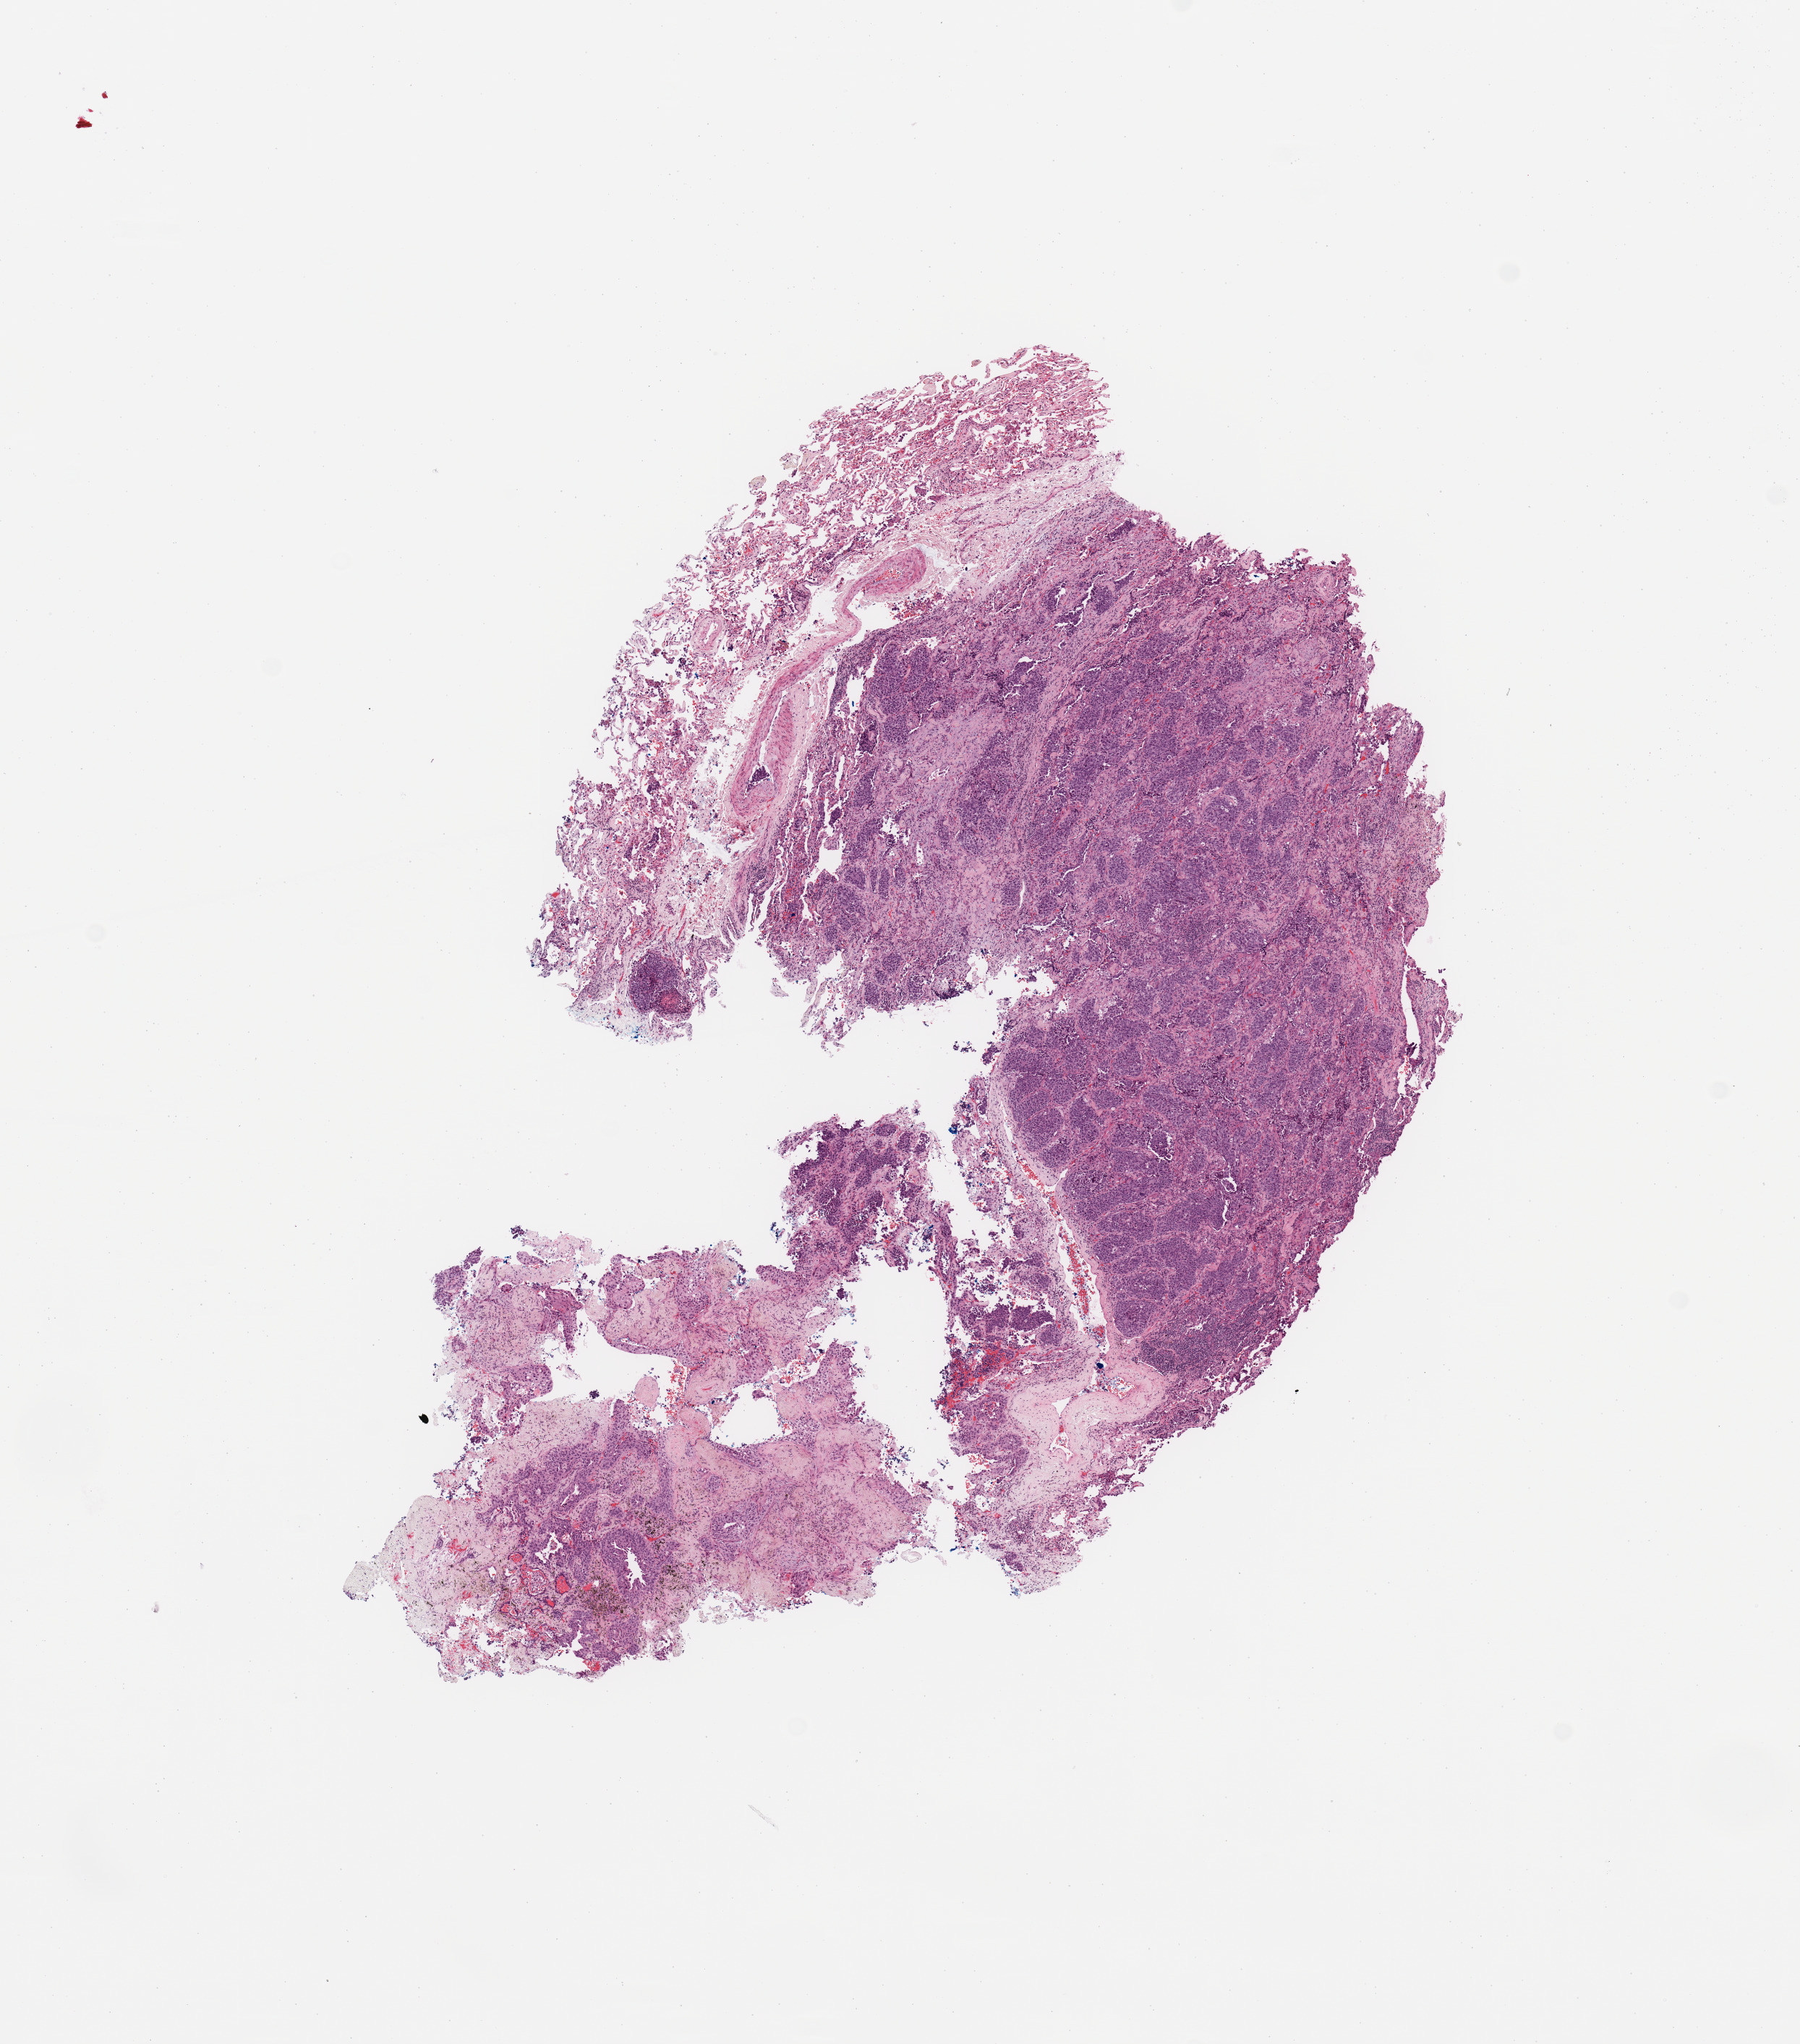
Digitized H&E-stained tissue section (whole slide), shown as a low-resolution overview of the whole scanned area (about 9.8 x 11.2 mm), tumour tissue sample, sampled site: lung. Patient: female, age 73 years. Histologic grade: G3 (poorly differentiated). Slide review estimates, as recorded: tumour nuclei 70%, necrosis 10%.
- primary tumour site (as recorded): right upper lobe
- histologic diagnosis: Squamous cell carcinoma, NOS
- AJCC pathologic stage: IIIA